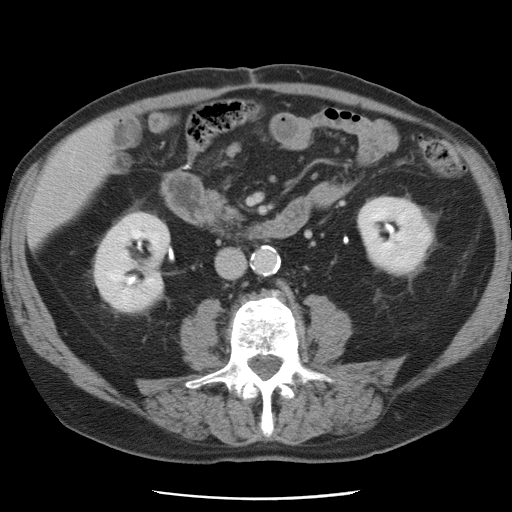
Contrast-enhanced abdominal CT, one axial slice; slice 18 of 78 in the series (ordered by position); intravenous contrast given; soft-tissue window (W 400 / L 40 HU); 5 mm slice thickness; 512 × 512 image matrix, field of view 337 × 337 mm. Male patient, age 75 years. From the clinical record (not read from this slice): diagnosis: colorectal cancer liver metastases, imaged before liver resection; multiple liver metastases: yes; largest metastasis: 2.4 cm; chemotherapy before resection: yes.
Structures marked on this image (expert manual segmentation):
- liver: bounding box (x1, y1, x2, y2) in pixels: (31, 123, 111, 242)
- planned liver remnant (the part of the liver to remain after resection): (30, 124, 111, 242)